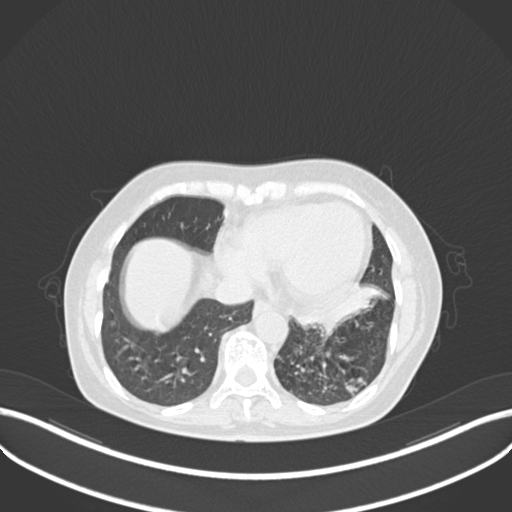
Chest CT, one axial slice; position 77 of 270 along the scan axis; reconstruction kernel B30f; 120 kVp; lung window (W 1500 / L -600 HU); 512 × 512 image matrix, field of view 400 × 400 mm. Female patient, age 63 years. Case-level facts recorded for this patient, not image findings: clinical TNM (as recorded): T1b N0 M0.
Structures marked on this image (bounding box drawn by a radiologist):
- lung tumour (recorded histology: adenocarcinoma): bounding box (x1, y1, x2, y2) in pixels: (295, 285, 388, 333)